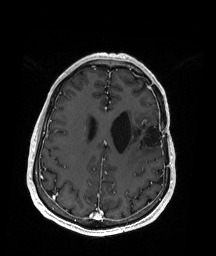
Brain MRI from a brain-tumour surgery series, one axial slice; slice 66 of 192 in the series (ordered by position); T1-weighted post-contrast; 1 mm slice thickness; 216 × 256 image matrix, field of view 211 × 250 mm. From the clinical record (not read from this slice): histopathology: Oligodendroglioma; WHO grade: 2; IDH mutation: yes.
Annotated regions visible in this slice (outlined manually by an expert reader):
- previous resection cavity: box from (x=132, y=122) to (x=163, y=146) px